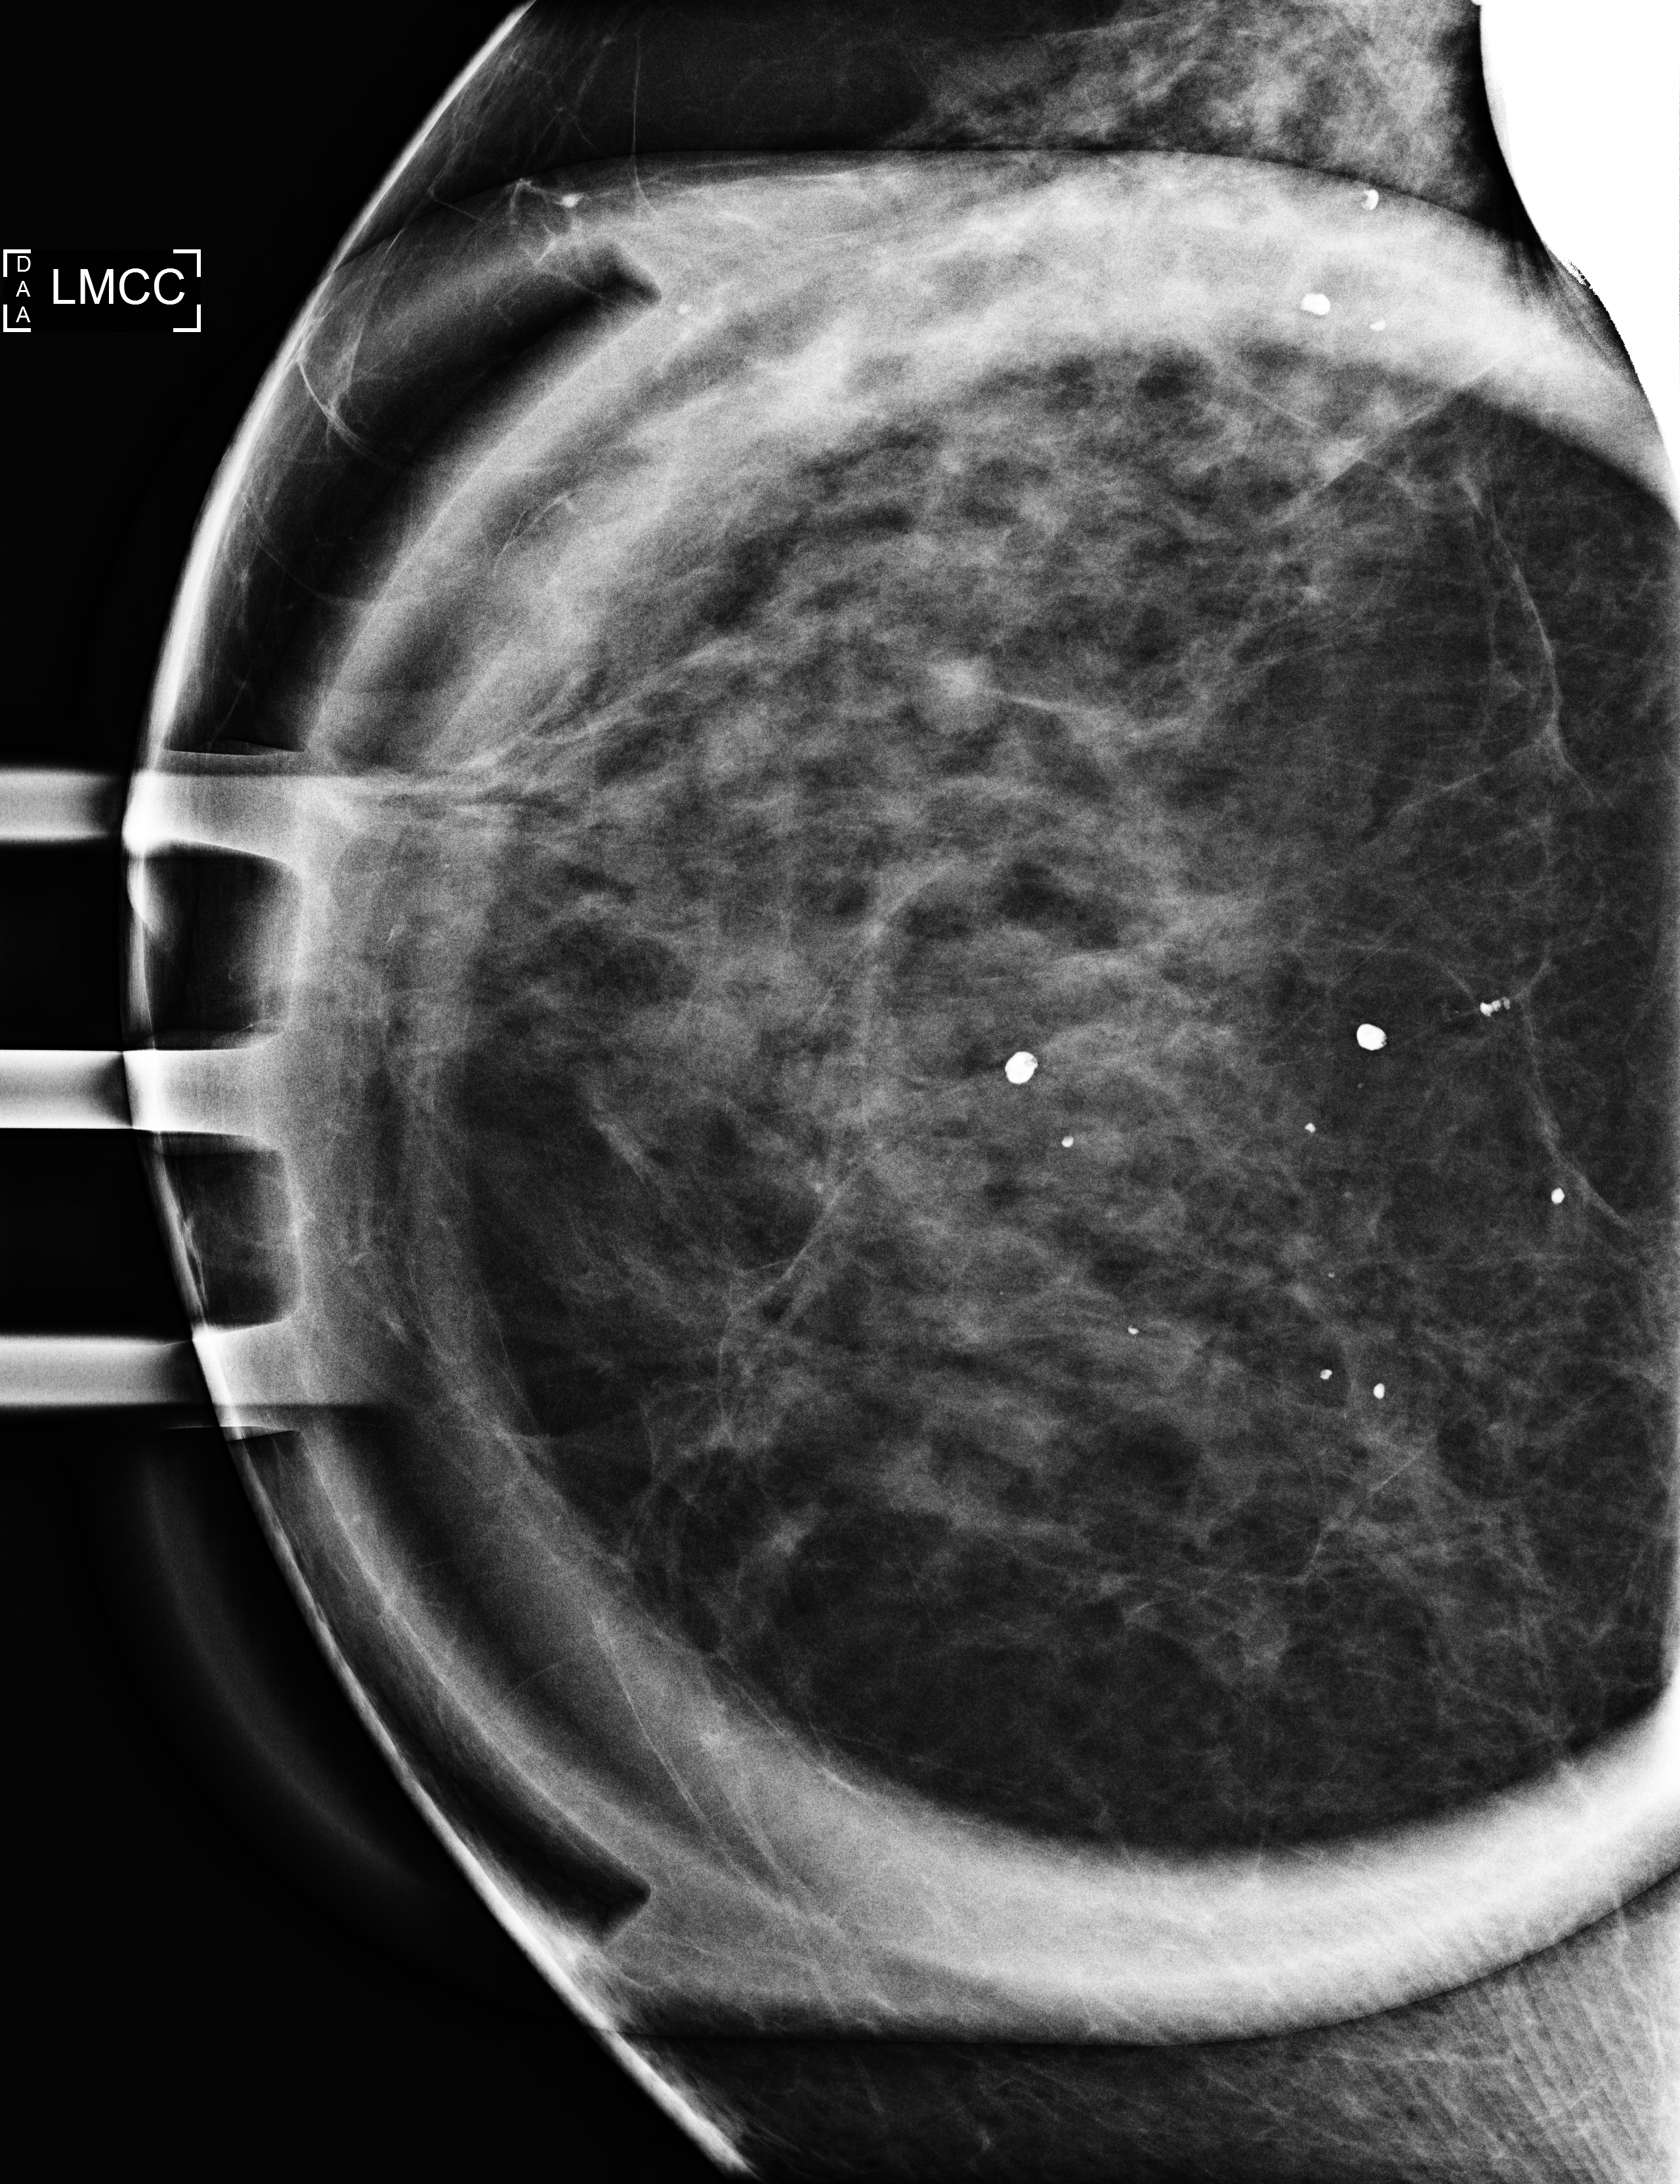
Digital mammogram (FFDM), left breast, craniocaudal (CC) view (magnification), additional (diagnostic) view, compressed breast thickness 50 mm. Patient aged 49 years (female).
- breast density at the screening exam (both breasts): heterogeneously dense (BI-RADS density category c)
- final BI-RADS category for the screening round (tomosynthesis exam, both breasts): category 2
- recall: recalled for additional imaging after this screen